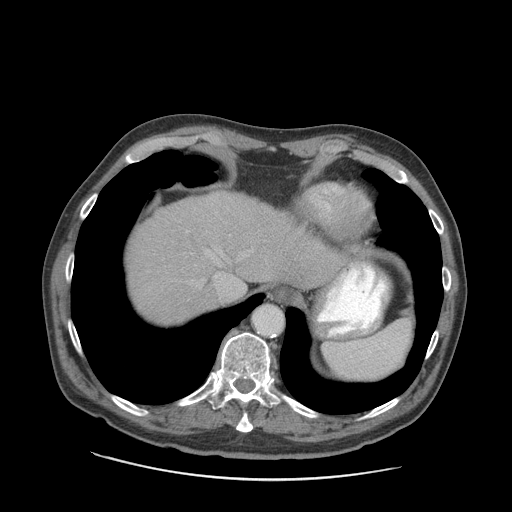
Contrast-enhanced abdominal CT (liver protocol), one axial slice; position 75 of 89 along the scan axis; soft-tissue window (W 400 / L 40 HU); 512 × 512 image matrix. From the clinical record (not read from this slice): diagnosis: hepatocellular carcinoma (patient treated with transarterial chemoembolisation; whether this scan precedes or follows treatment is not stated here); TNM stage (as recorded): Stage-I; Child-Pugh class: A; tumour differentiation: moderately differentiated; tumour nodularity: uninodular.
Outlined on this slice (semi-automatically segmented with operator editing):
- abdominal aorta: bounding box (x1, y1, x2, y2) in pixels: (253, 305, 283, 335)
- liver parenchyma outside the tumour (the mass and vessels are separate outlines, so this box may not span the whole liver): (128, 192, 345, 324)
- liver vessels: (186, 230, 244, 291)